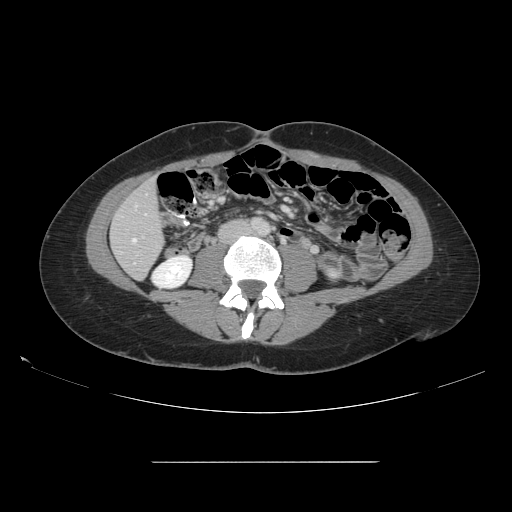
Contrast-enhanced abdominal CT, one axial slice. Position 32 of 151 along the scan axis. Soft-tissue window (W 400 / L 40 HU). 2.5 mm slice thickness. 512 × 512 image matrix, field of view 421 × 421 mm. Female patient, age 46 years. From the clinical record (not read from this slice): diagnosis: colorectal cancer liver metastases, imaged before liver resection; multiple liver metastases: yes; largest metastasis: 3 cm; disease in both lobes: yes.
Outlined on this slice (manually delineated by an expert):
- hepatic veins: bounding box <133,239,136,242> (left, top, right, bottom; pixels)
- liver: <112,181,164,279>
- planned liver remnant (the part of the liver to remain after resection): <112,181,164,279>